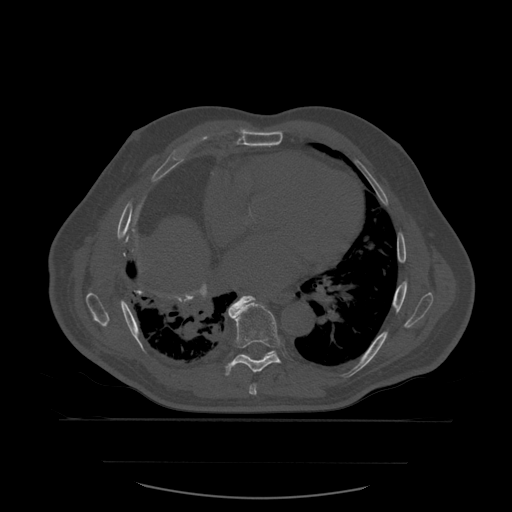
CT including the spine, one axial slice. Slice 360 of 590 in the series (ordered by position). Bone window (W 1800 / L 400 HU). 1.25 mm slice thickness. 512 × 512 image matrix. Patient age 71 years. Case-level facts recorded for this patient, not image findings: primary cancer: lung; vertebrae with lytic lesions (as recorded): T1, T2, L5, S1.
Annotated regions visible in this slice (semi-automatically segmented with operator editing):
- T7 vertebra: bounding box [x1, y1, x2, y2] px = [249, 384, 257, 395]
- T8 vertebra: [226, 296, 281, 376]
- T9 vertebra: [265, 351, 274, 356]